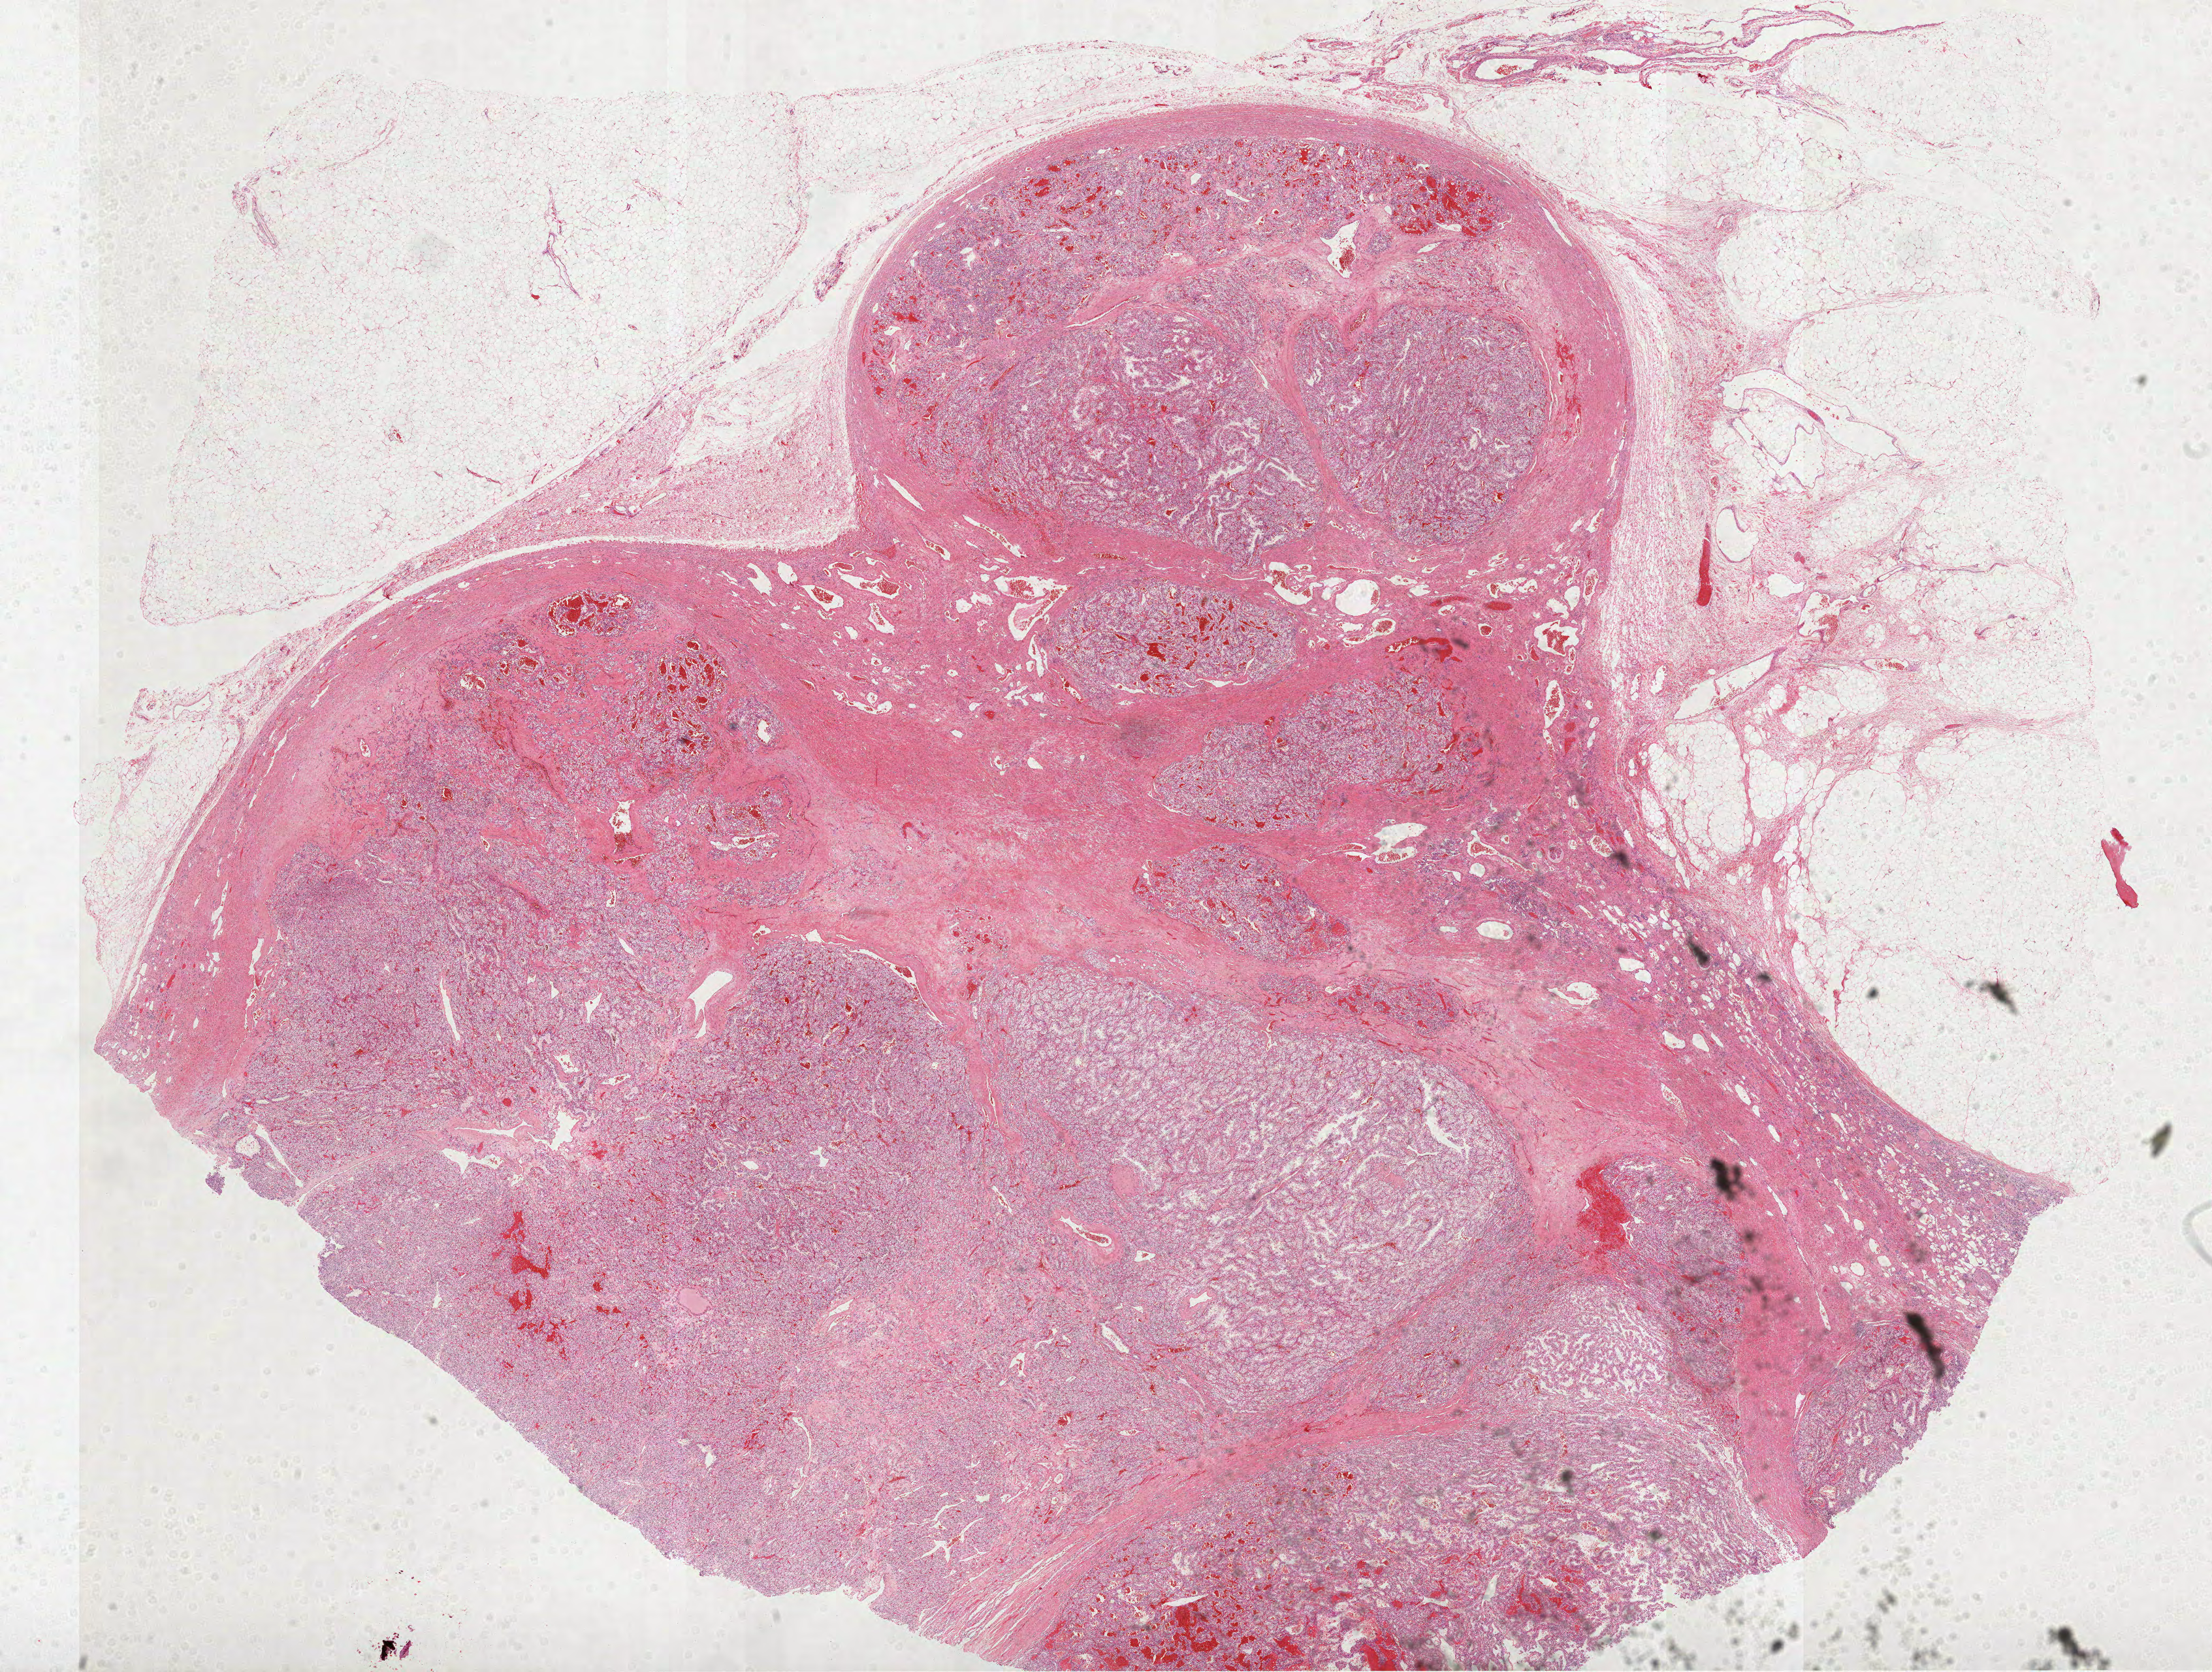
Whole-slide histology image, H&E-stained — shown as a low-resolution overview of the whole scanned area (about 27.3 x 20.6 mm). FFPE section. Primary tumour sample from the kidney. Male patient; age at initial diagnosis 64 years. Histologic grade: G2 (moderately differentiated).
- histologic diagnosis: Clear cell adenocarcinoma, NOS
- AJCC pathologic stage: I
- laterality: left